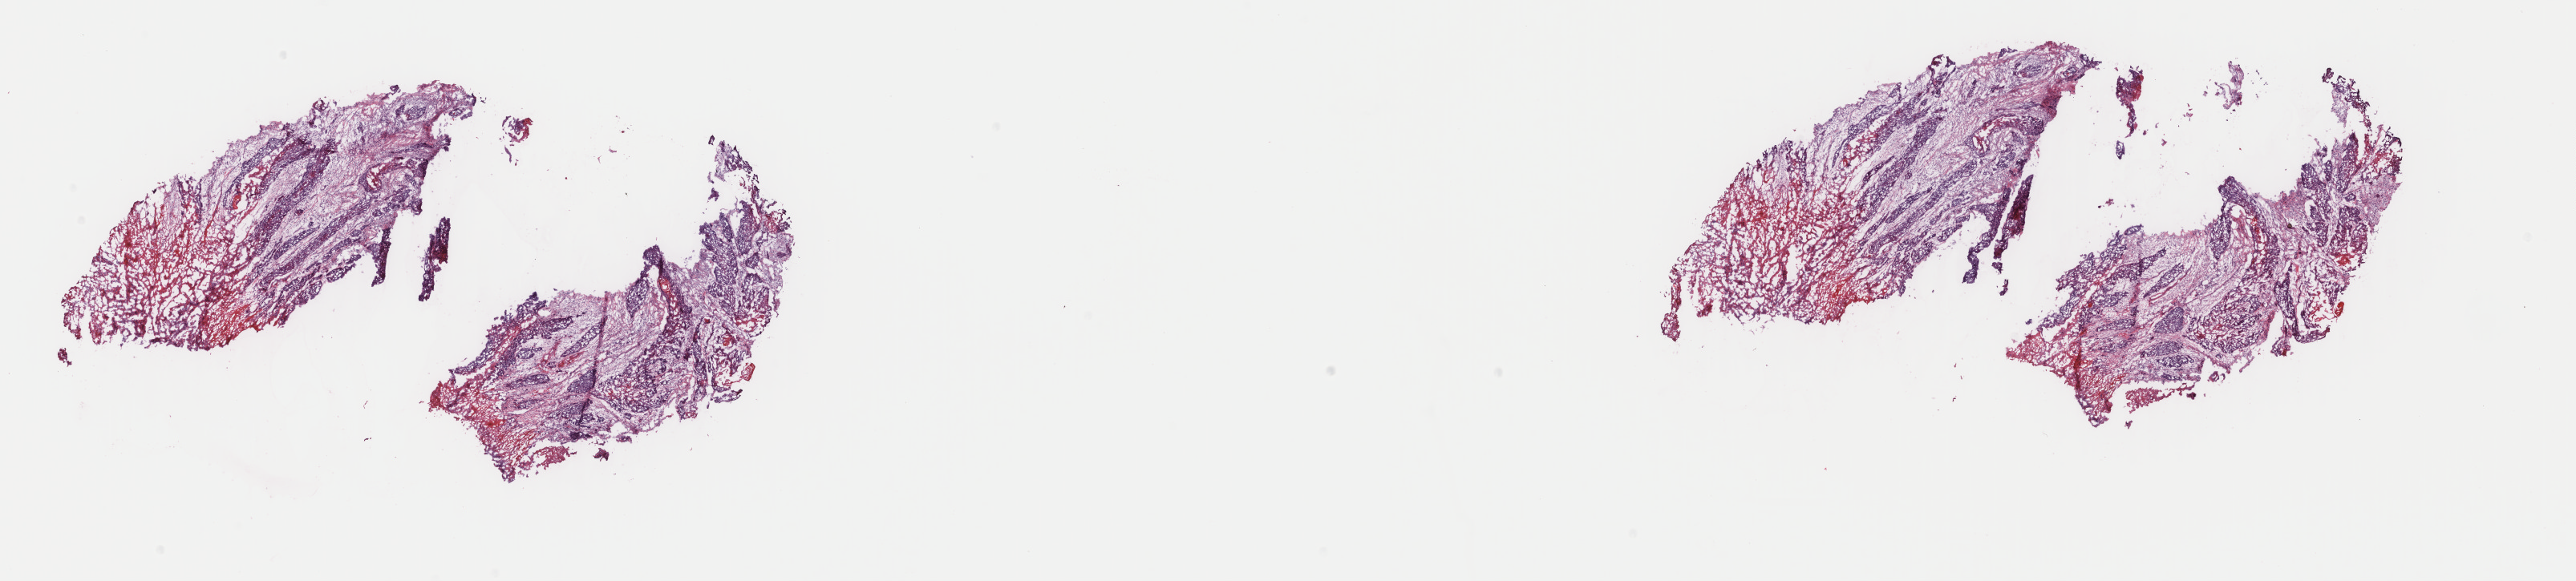
H&E whole-slide image — shown as a low-resolution overview of the whole scanned area (about 25.5 x 5.8 mm); frozen section from the top of the tissue portion; sample: primary tumour, head and neck. Female patient; age at initial diagnosis 66 years. Histologic grade: G2 (moderately differentiated). Composition of this section per pathologist review: tumour cells 60%, tumour nuclei 60%, normal cells 0%, stromal cells 40%, necrosis 0%. Inflammatory infiltration, as recorded: lymphocyte infiltration 5%, monocyte infiltration 0%, neutrophil infiltration 0%.
- TNM: T4a N1 M0
- diagnosis: Squamous cell carcinoma, NOS (cheek mucosa)
- AJCC pathologic stage: IVA